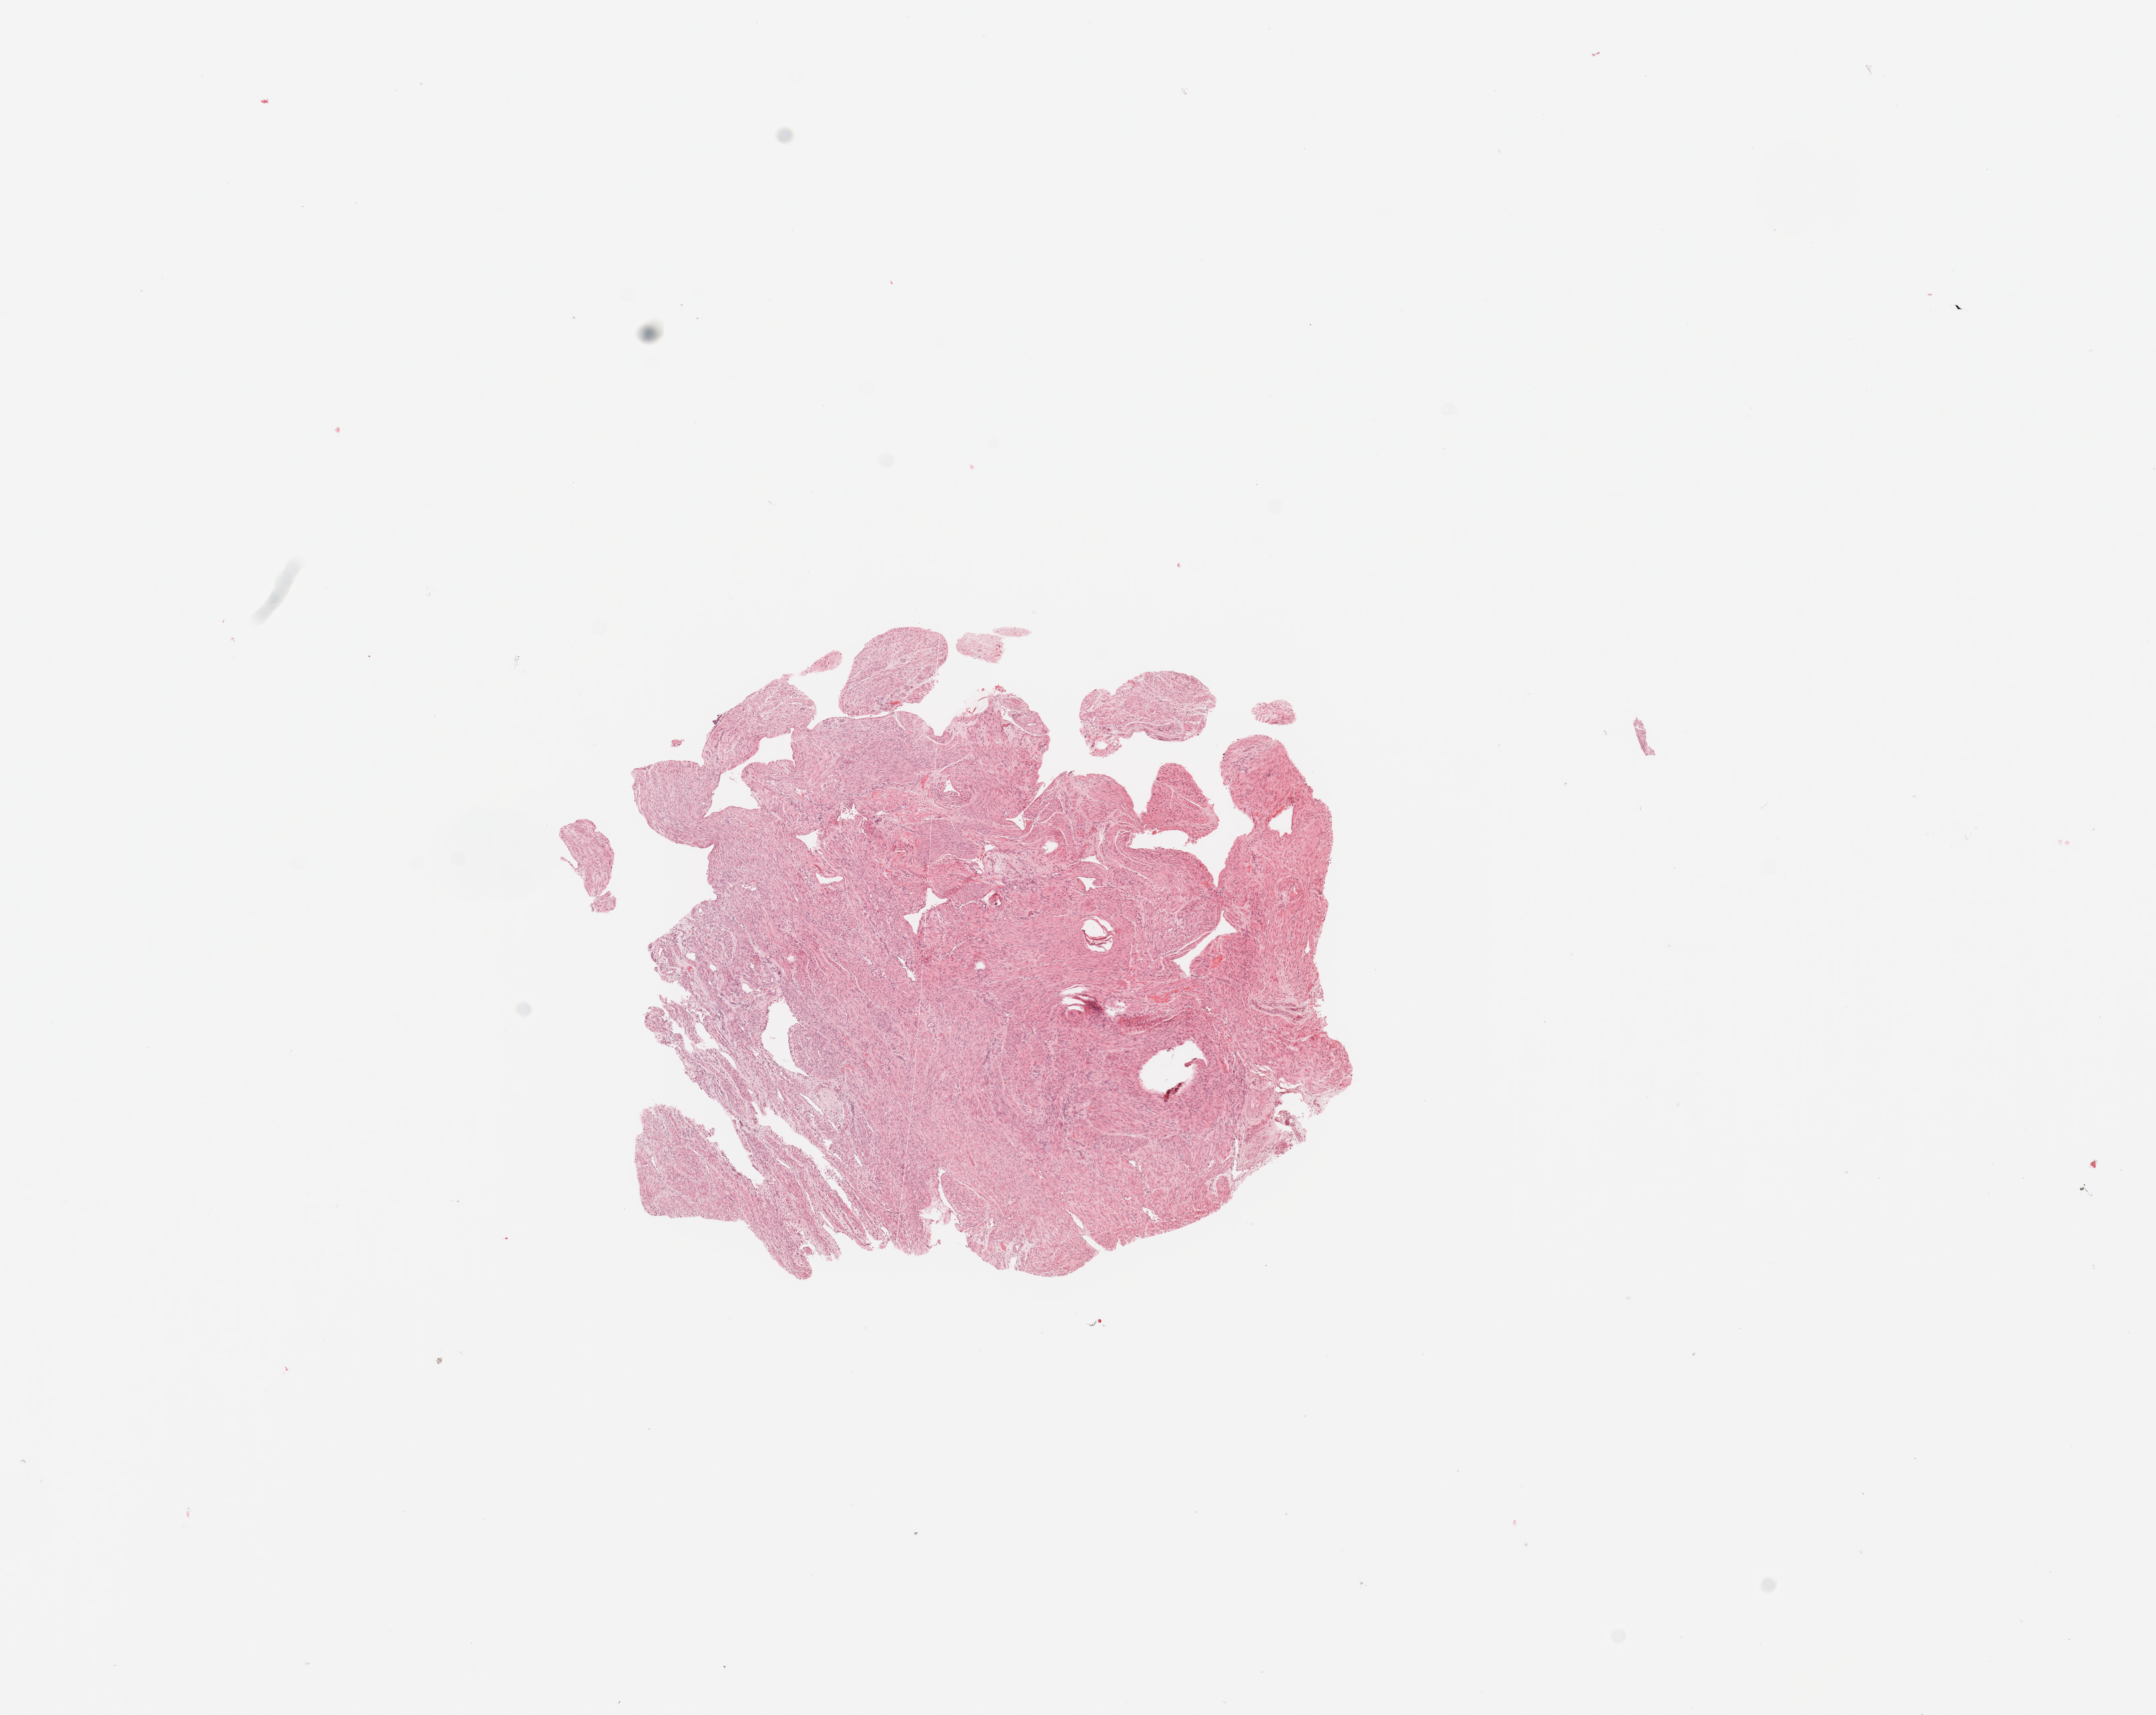
Digitized H&E-stained tissue section (whole slide), shown as a low-resolution overview of the whole scanned area (about 12.8 x 10.2 mm, from a 20x scan); normal (non-tumour) tissue sample, uterus. Patient: female, age 66 years.
* this section: normal (non-tumour) tissue from the same patient
* patient diagnosis: Endometrioid adenocarcinoma, NOS